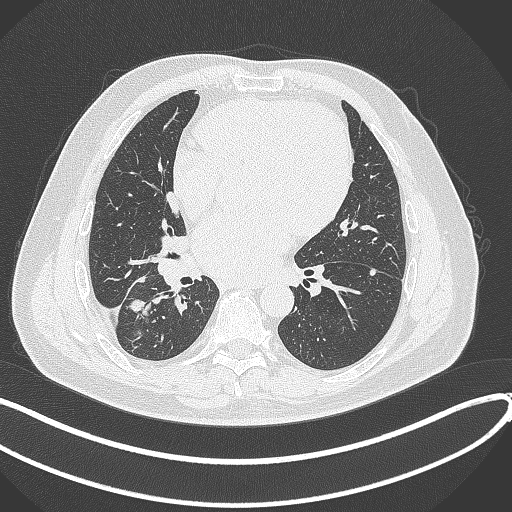
Chest CT, one axial slice; slice 169 of 360 in the series (ordered by position); 120 kVp; lung window (W 1500 / L -600 HU); 1 mm slice thickness; 512 × 512 image matrix, field of view 400 × 400 mm. Patient: male, 59 years.
Annotated regions visible in this slice (bounding box drawn by a radiologist):
- lung tumour (recorded histology: adenocarcinoma): box from (x=126, y=296) to (x=154, y=319) px